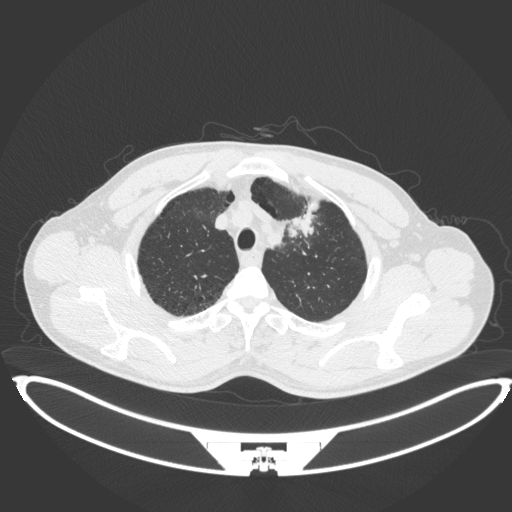
Chest CT, one axial slice; position 367 of 407 along the scan axis; reconstruction kernel B31f; 120 kVp; lung window (W 1500 / L -600 HU); 512 × 512 image matrix, field of view 457 × 457 mm. Patient: male, 60 years. Case-level facts recorded for this patient, not image findings: clinical TNM (as recorded): T2a N0 M0; histopathological grade: G1-G2.
Outlined on this slice (rectangle marked by the reading radiologist):
- lung tumour (recorded histology: squamous cell carcinoma): box from (x=285, y=203) to (x=319, y=240) px